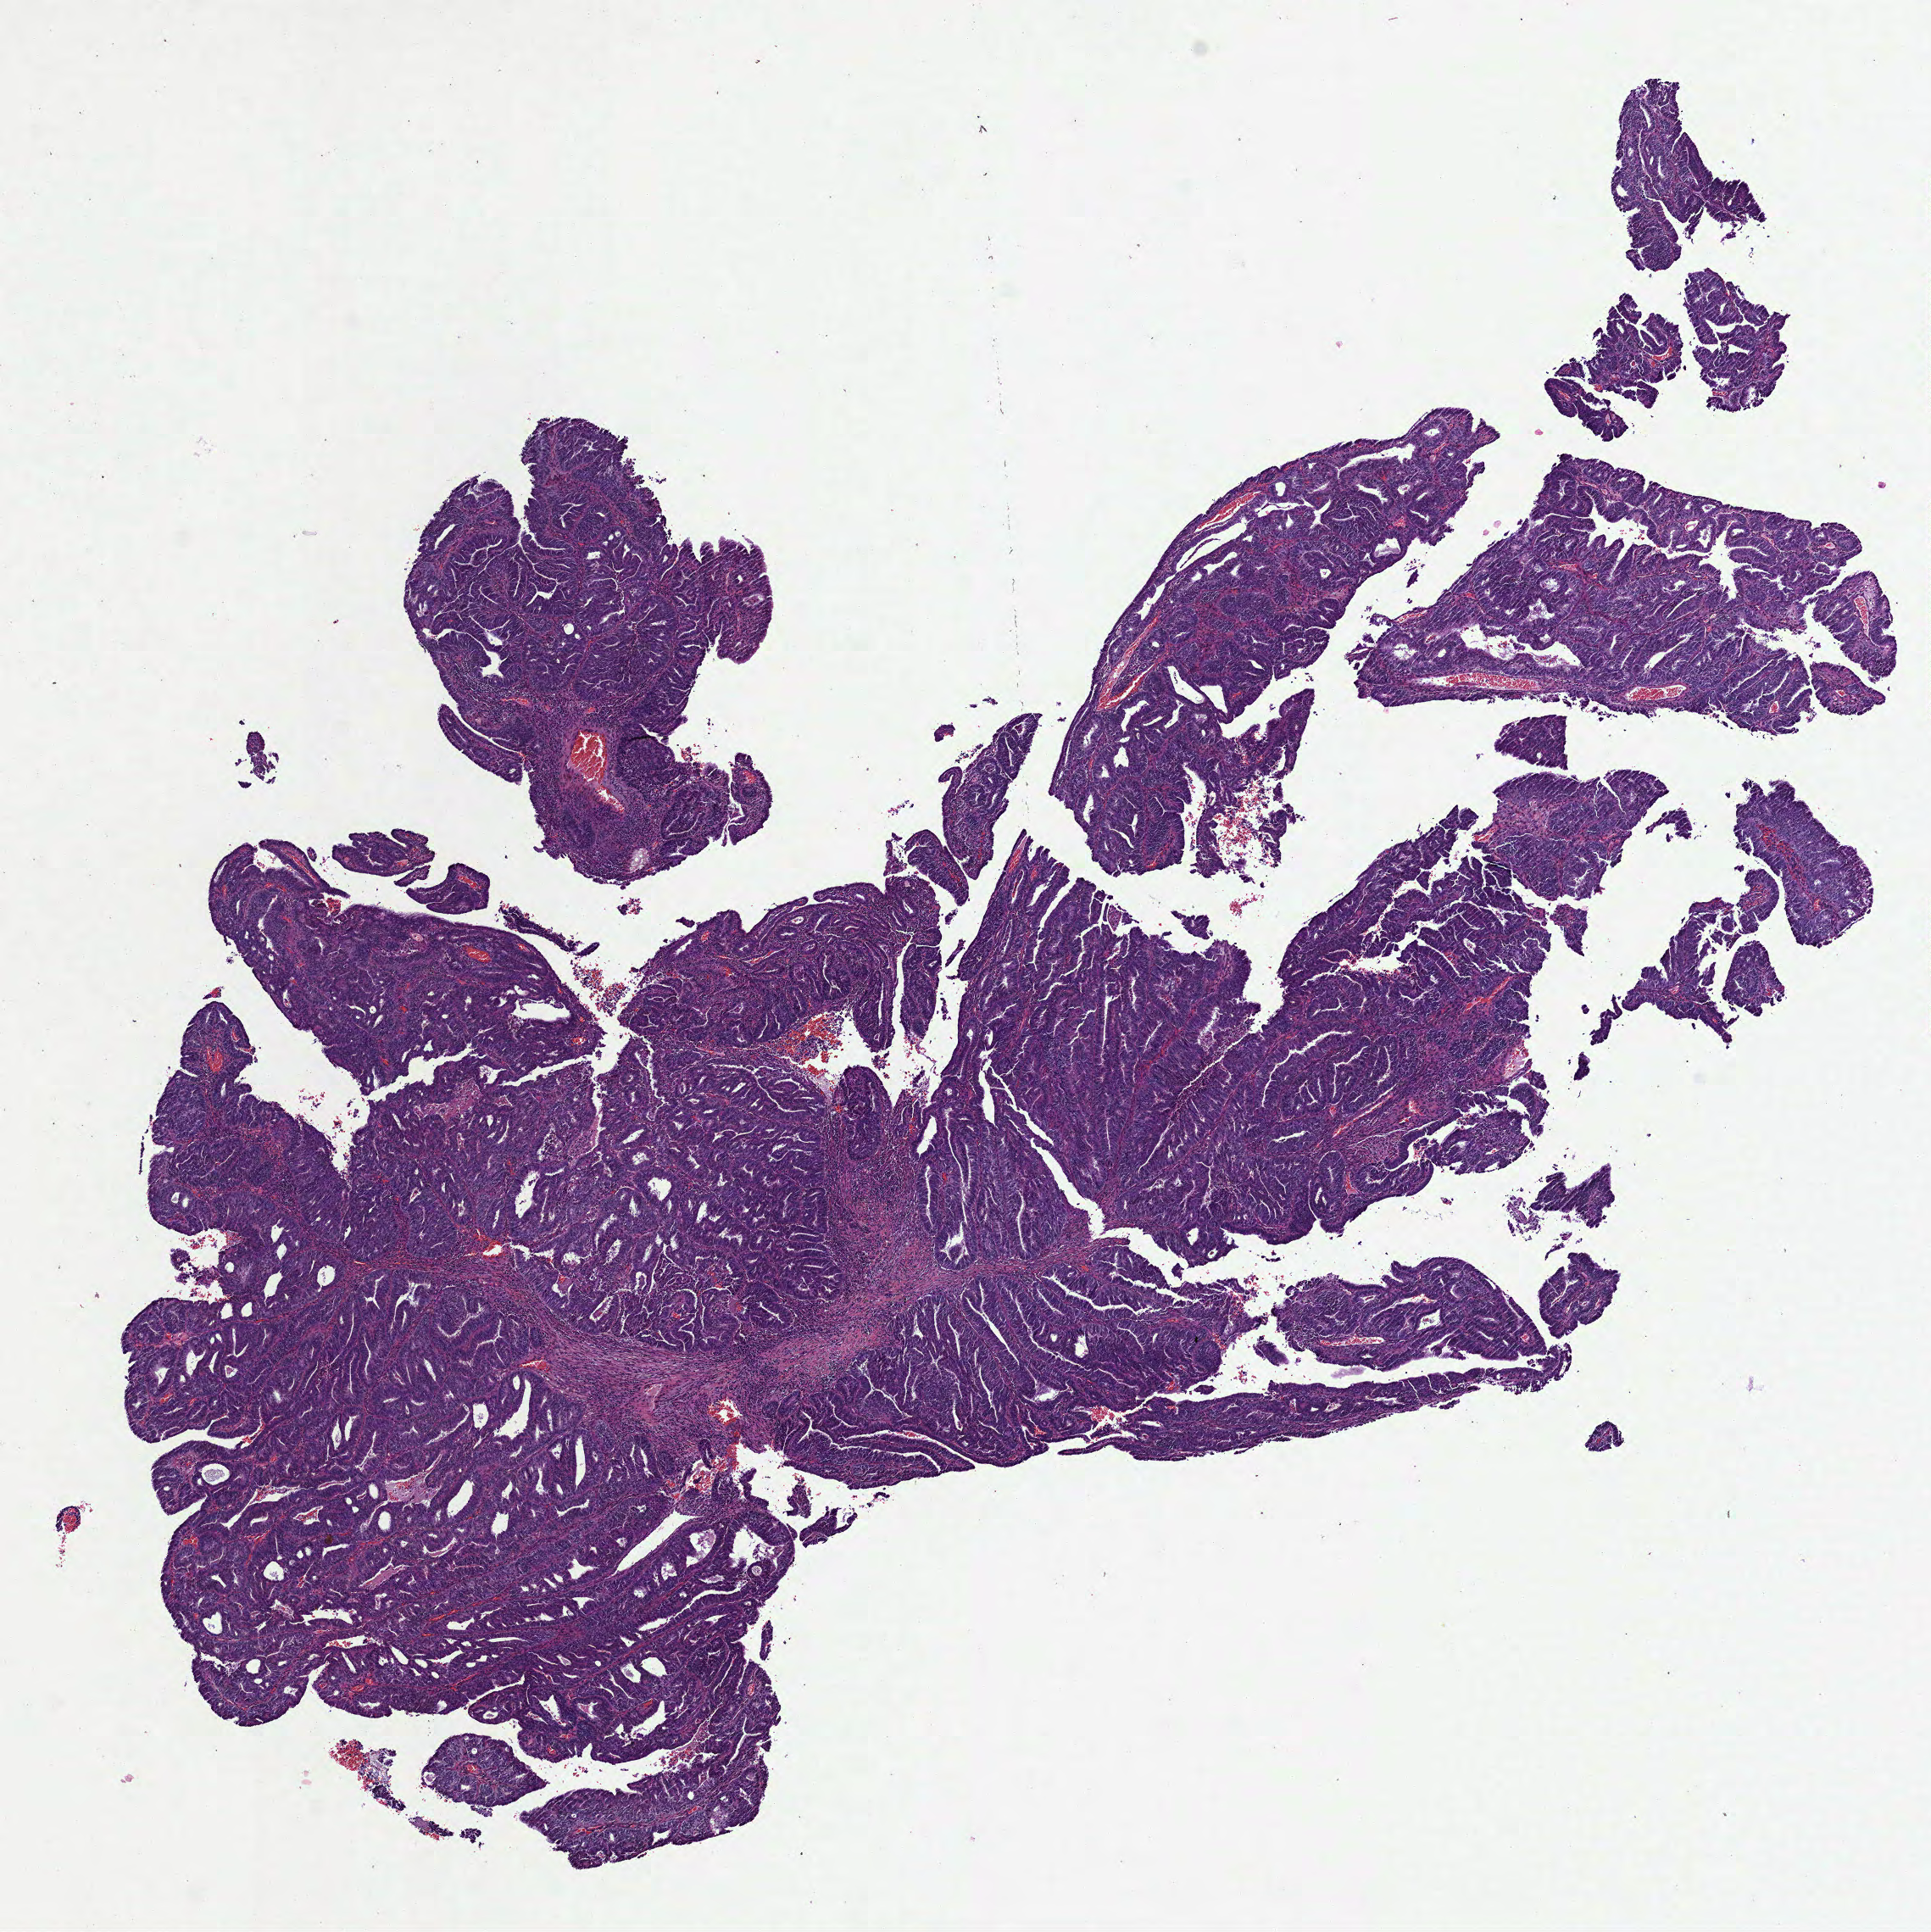
Whole-slide histology image, Hematoxylin and eosin (H&E) stained — whole scanned area (about 9.2 x 9.2 mm, slide scanned at 40x) shown as a low-resolution overview; formalin-fixed paraffin-embedded (FFPE) diagnostic section; uterus, primary tumour sample. Patient: female, age at initial diagnosis 56 years. Histologic grade: G2 (moderately differentiated).
FIGO stage: IA. Pathologic diagnosis: Endometrioid adenocarcinoma, NOS (endometrium). Lymph nodes positive (case pathology): 0 of 13 examined.